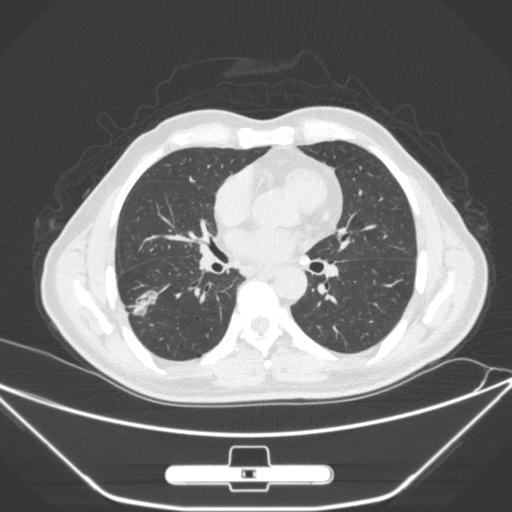
Chest CT, one axial slice; 120 kVp; lung window (W 1500 / L -600 HU); 1 mm slice thickness; 512 × 512 image matrix, field of view 398 × 398 mm. Male patient, age 71 years. Case-level facts recorded for this patient, not image findings: clinical TNM (as recorded): T1c N0 M0; histopathological grade: G2.
Structures marked on this image (bounding box drawn by a radiologist):
- lung tumour (recorded histology: adenocarcinoma): bounding box [x1, y1, x2, y2] px = [129, 286, 163, 321]